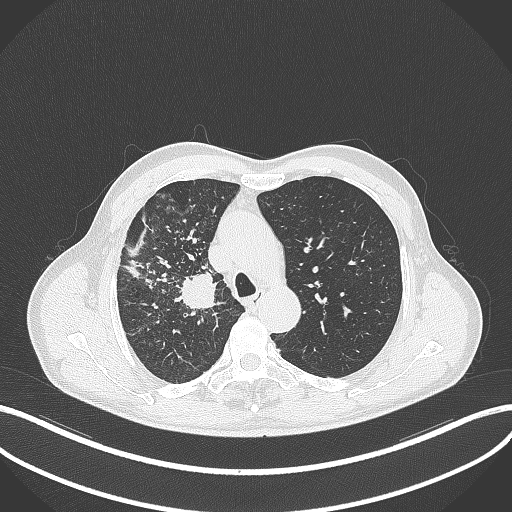
Chest CT, one axial slice. Slice 348 of 490 in the series (ordered by position). Reconstruction kernel B70f. 120 kVp. Lung window (W 1500 / L -600 HU). 512 × 512 image matrix, field of view 400 × 400 mm. Male patient, age 69 years. From the clinical record (not read from this slice): clinical TNM (as recorded): T2a N0 M0.
Annotated regions visible in this slice (rectangle marked by the reading radiologist):
- lung tumour (recorded histology: adenocarcinoma): bounding box (x1, y1, x2, y2) in pixels: (175, 269, 219, 311)